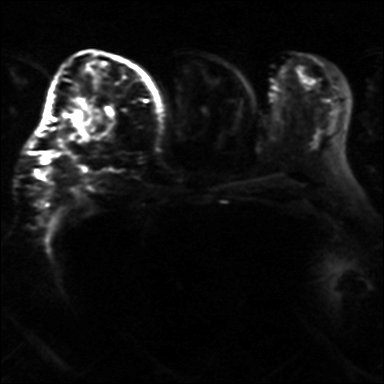
Breast MRI, one axial slice; position 19 of 36 along the scan axis; diffusion-weighted series; image 2 of 4 stored at this slice position (different b-values; order by instance number); 3 T; 4 mm slice thickness; 384 × 384 image matrix, field of view 320 × 320 mm. Female patient.
Outlined on this slice (outlined manually by an expert reader):
- tumour on diffusion-weighted imaging: bounding box [x1, y1, x2, y2] px = [73, 115, 86, 131]